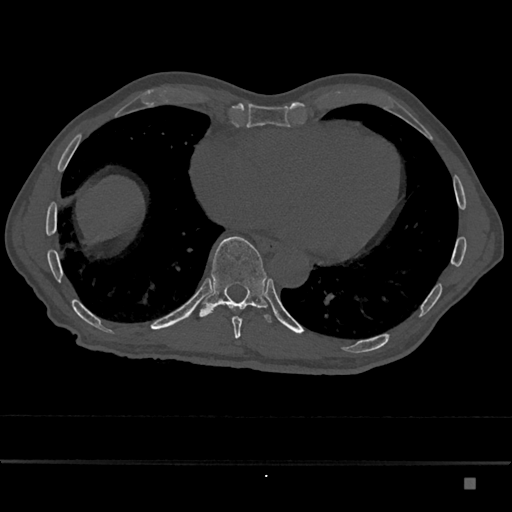
CT including the spine, one axial slice. Position 764 of 797 along the scan axis. Reconstruction kernel Br40s/3. 120 kVp. Bone window (W 1800 / L 400 HU). 0.5 mm slice thickness. 512 × 512 image matrix. Patient: male, 72 years. Case-level facts recorded for this patient, not image findings: primary cancer: prostate.
Outlined on this slice (semi-automatic segmentation, software-assisted and operator-edited):
- T10 vertebra: bounding box <199,236,272,323> (left, top, right, bottom; pixels)
- T9 vertebra: <232,309,243,339>